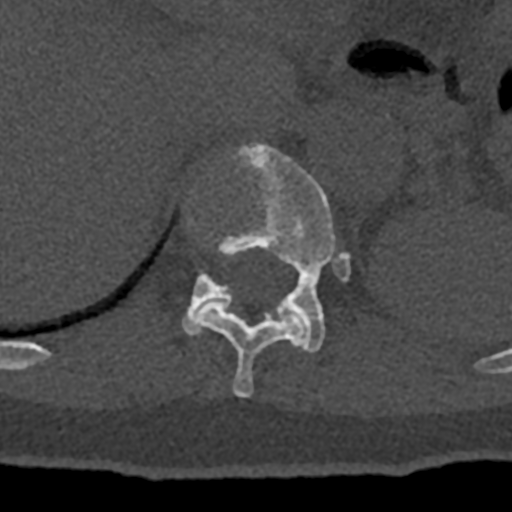
CT including the spine, one axial slice. Slice 521 of 797 in the series (ordered by position). Bone window (W 1800 / L 400 HU). 0.5 mm slice thickness. 512 × 512 image matrix, field of view 160 × 160 mm. Patient: male, 74 years. From the clinical record (not read from this slice): primary cancer: renal; vertebrae with lytic lesions (as recorded): T10, L1, L2, L3, L4, L5.
Annotated regions visible in this slice (semi-automatic segmentation, software-assisted and operator-edited):
- T11 vertebra: box from (x=193, y=301) to (x=307, y=398) px
- T12 vertebra: (x=182, y=142)–(x=350, y=353)